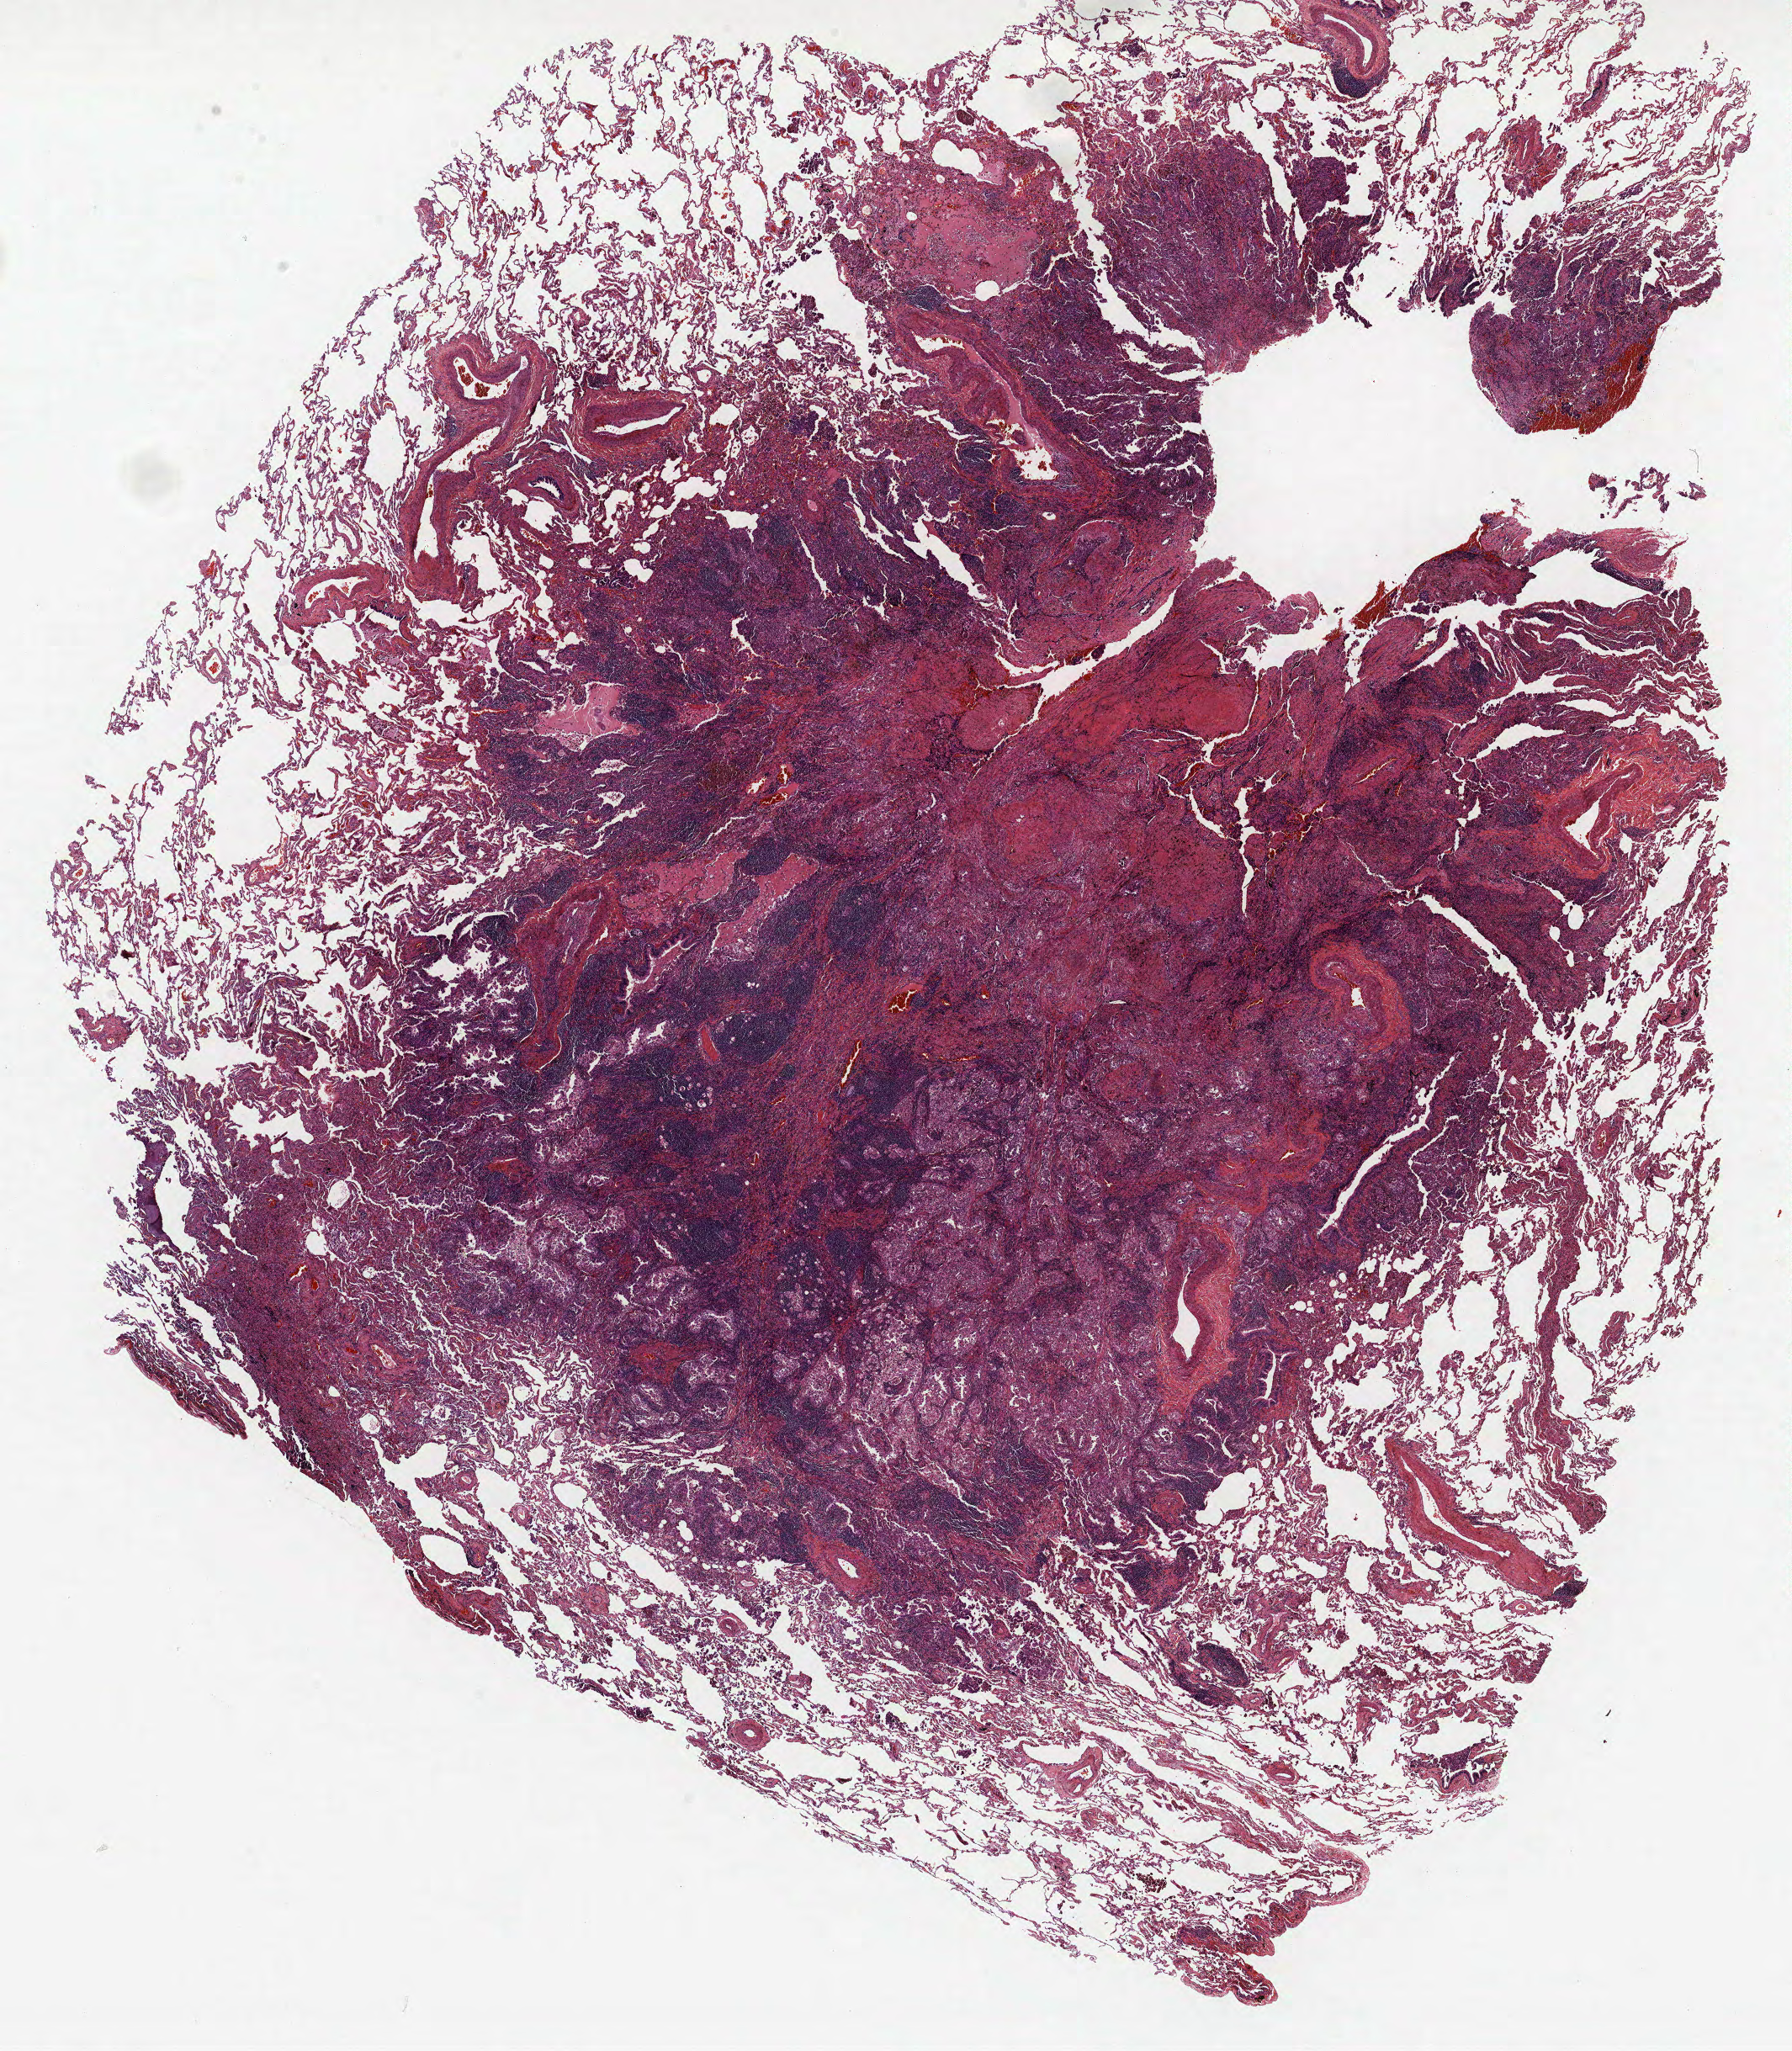
H&E whole-slide image — low-resolution overview of the scanned area, about 17.0 x 19.5 mm; formalin-fixed paraffin-embedded (FFPE) section; lung tissue. Male patient, aged 63 at enrolment. Current smoker at enrolment.
Participant's lung-cancer diagnosis: Adenocarcinoma, NOS.